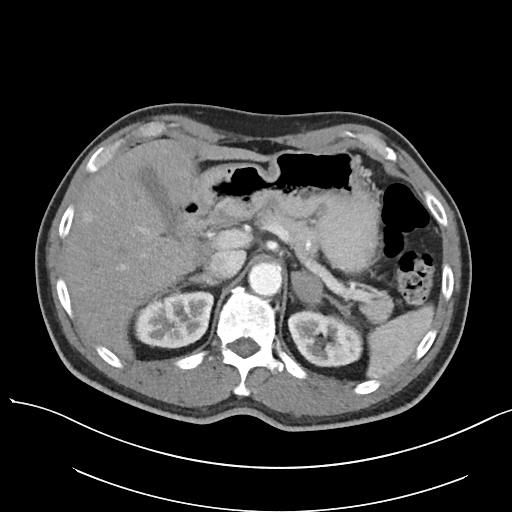
Contrast-enhanced abdominal CT, one axial slice. Position 78 of 138 along the scan axis. Intravenous contrast given. Soft-tissue window (W 400 / L 40 HU). 5 mm slice thickness. 512 × 512 image matrix. Male patient, age 63 years. Case-level facts recorded for this patient, not image findings: diagnosis: adrenocortical carcinoma; tumour side: left adrenal; tumour size at pathology: 4.5 cm; Ki-67 index: 12 %; stage (as recorded): 1.
Outlined on this slice (semi-automatic segmentation, software-assisted and operator-edited):
- mass: box from (x=291, y=269) to (x=322, y=303) px